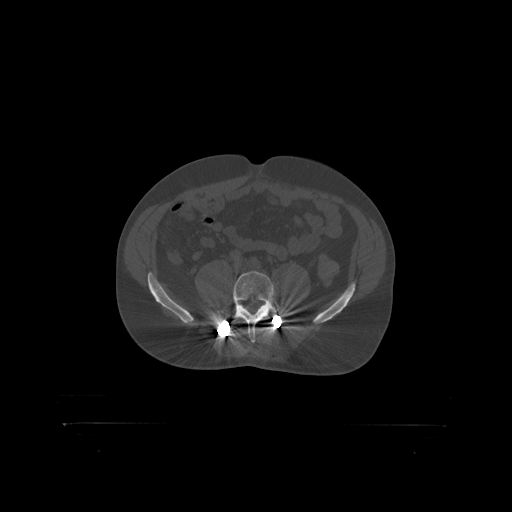
CT including the spine, one axial slice; slice 207 of 399 in the series (ordered by position); bone window (W 1800 / L 400 HU); 1.25 mm slice thickness; 512 × 512 image matrix, field of view 650 × 650 mm. Male patient, age 46 years. From the clinical record (not read from this slice): primary cancer: skin.
Outlined on this slice (semi-automatic segmentation, software-assisted and operator-edited):
- L5 vertebra: box from (x=228, y=271) to (x=281, y=319) px